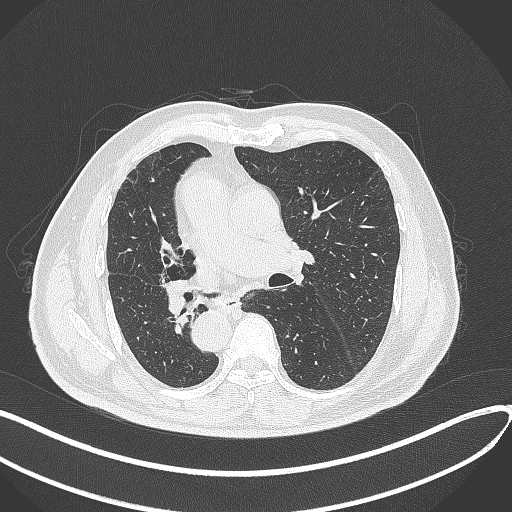
Chest CT, one axial slice. Slice 155 of 300 in the series (ordered by position). Reconstruction kernel B70f. Lung window (W 1500 / L -600 HU). 512 × 512 image matrix, field of view 400 × 400 mm. Male patient, age 67 years. Case-level facts recorded for this patient, not image findings: clinical TNM (as recorded): T2a N0 M0.
Annotated regions visible in this slice (bounding box drawn by a radiologist):
- lung tumour (recorded histology: squamous cell carcinoma): box from (x=158, y=280) to (x=190, y=316) px